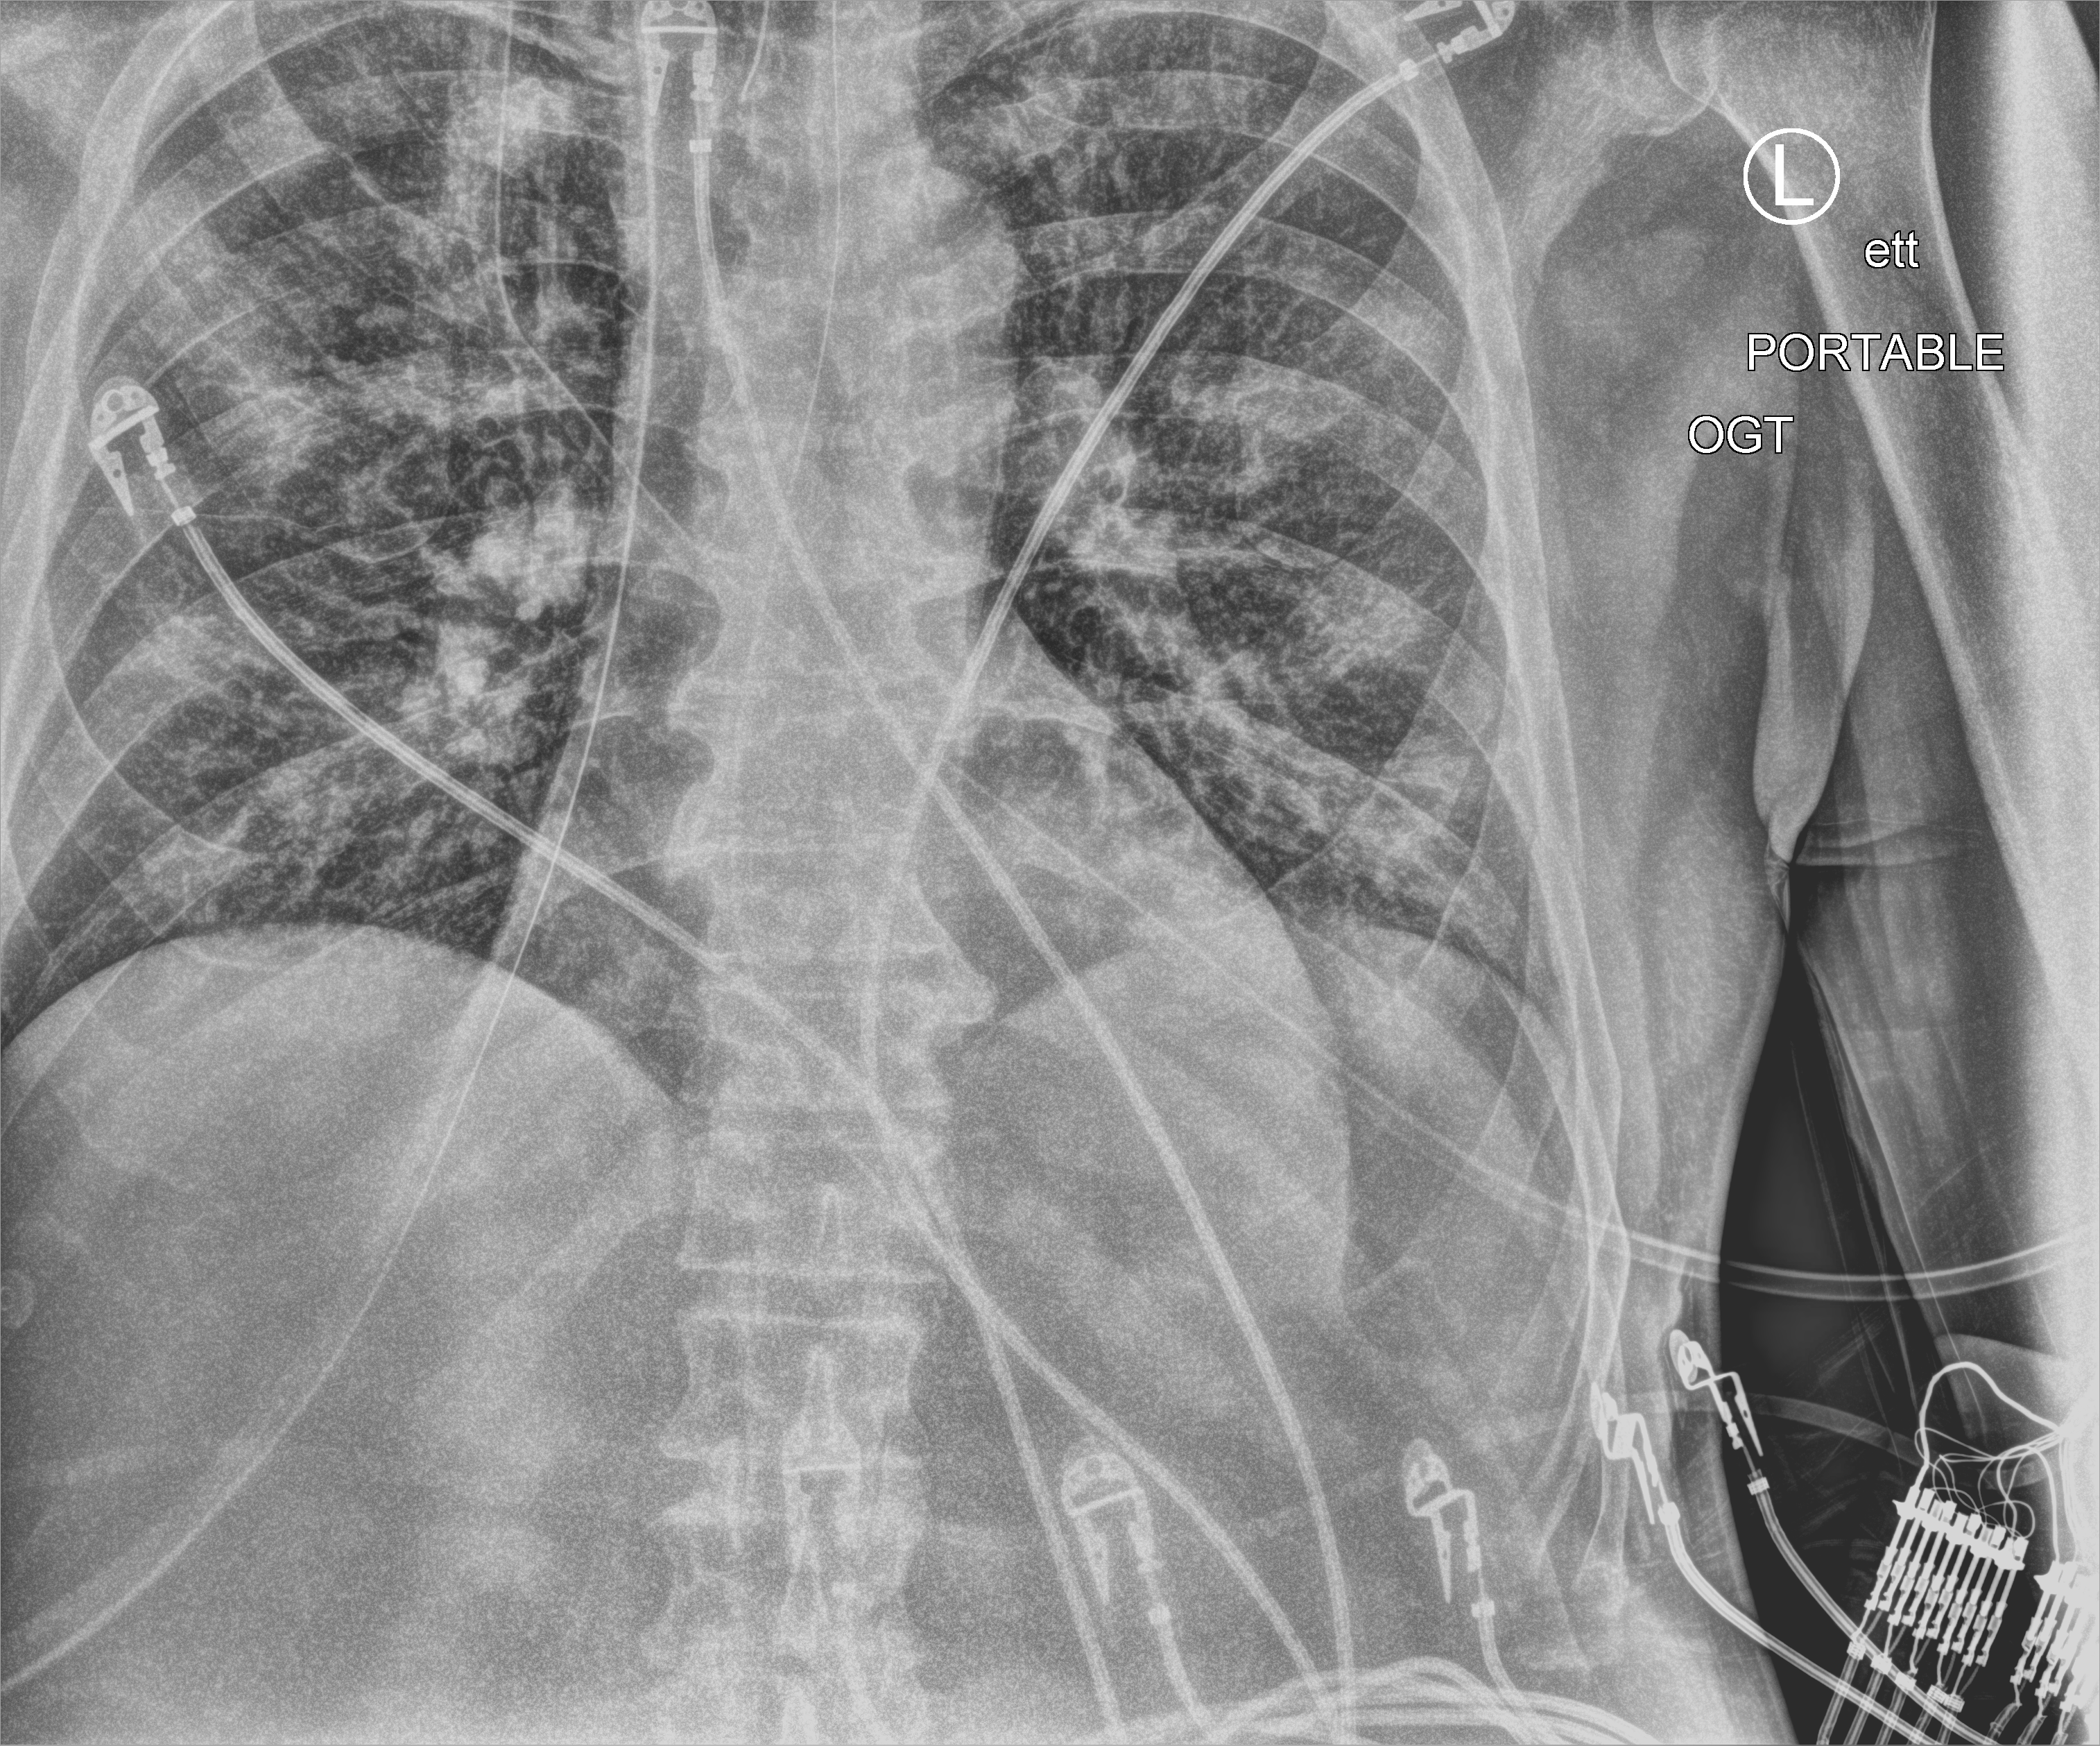
Portable chest radiograph. Male patient hospitalised with COVID-19, age 60–74 years.
Hospital-stay facts (about this admission, not read from this image; timing relative to this image not recorded):
- admitted to intensive care during this hospital stay: yes
- mechanically ventilated during this hospital stay: yes